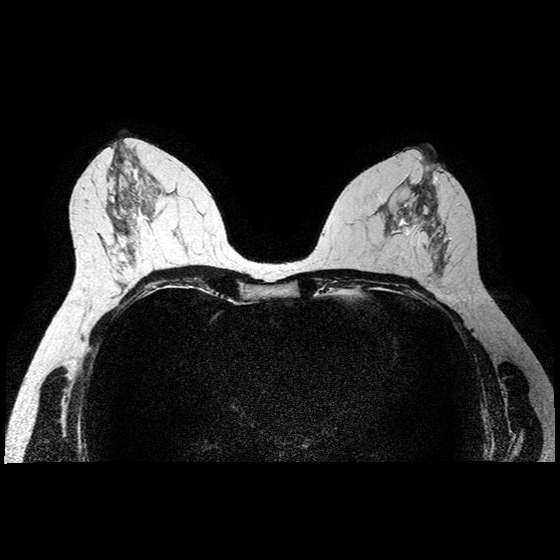
MRI of the breasts; 2 images, each one mid-volume slice chosen by position. Age decade 40s.
Image 1: axial T2-weighted / STIR image, series "T2W_TSE SENSE", slice 43 of 84.
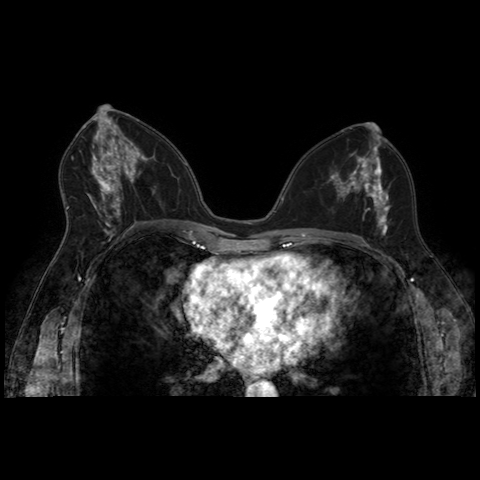
Image 2: post-contrast dynamic axial slice, slice 43 of 84, dynamic phase 5 of 8, 4 mm slice thickness.
MRI impression (as recorded): LEFT BREAST: There is moderate background enhancement. In the leftcentral slightly lateral breast mid depth, 2.4 cm from the nipple and 1.7 cm from the skin there is a 3.4 x 1.5 x 2.3 cm suspiciously enhancing mass seen (volume 2.8 cc), irregularly shaped and spiculated with centrally rapid wash in and washout pattern (Type 3). Posterior tothis dominant lesion there is a second 1.3 x 0.5 x 0.96 cm suspiciously enhancing (Type 3) focus of enhancement seen (5.6 cm from the nipple and 1.9 cm from the skin). Anterior to the dominant lesion there are small areas of suspicious enhancement seen up to 0.9 cm from the nipple. The total anterior posterior extension of the enhancing masses and foci is 5.4 cm in linear order towards the nipple (0.9 cm distance from nipple) and the maximal lateral is 2.5 cm. There is nipple inversion. There is no skin thickening, or left axillary lymphadenopathy present. Benign up to 8 mm simple cysts.
RIGHT BREAST: There is moderate background enhancement. No foci of suspicious enhancement, masses, or areas of architectural distortion seen within the right breast. There is no skin thickening, nipple inversion, or right axillary lymphadenopathy present. Benign simple up to 12 mm cysts. IMPRESSION: 1) 3.5 cm suspicious mass in the left central breast. In addition second 1.3 cm focus of suspicious enhancement posterior to the dominant lesion, as detailed above. Total anterior posterior extension of enhancing mass smaller foci is 5.4 cm towards the nipple (9 mm) in linear configuration - and maximal lateral extension is 2.5 cm (significant images and detailed portfolio with post processed images are saved on PACS for review; raw images: series 705 slice location 84-100).) 2) Left nipple inversion. 3) No axillary lymphadenopathy, no evidence for pectoral muscle involvement. 4) No evidence of contralateral disease; BI-RADS 5.
Pathology recorded for this patient (not read from these images): pathology diagnosis: INVASIVE LOBULAR CARCINOMA. SIZE OF INVASIVE COMPONENT: 4x4x2cm (left breast); pathology report notes: INVASIVE LOBULAR CARCINOMA. SIZE OF INVASIVE COMPONENT: 4x4x2cm HISTOLOGIC MODIFIED SCARF BLOOM RICHARDSON GRADE: I/III LESS THAN 5% OF DUCTAL AND LOBULAR CARCINOMA IN-SITU PRESENT. PERINEURAL INVASION IS PRESENT. MARGINS ARE NEGATIVE FOR CARCINOMA. INVASIVE LOBULAR CARCINOMA. SIZE OF INVASIVE COMPONENT: 4x4x2cm HISTOLOGIC MODIFIED SCARF BLOOM RICHARDSON GRADE: I/III LESS THAN 5% OF DUCTAL AND LOBULAR CARCINOMA IN-SITU PRESENT. PERINEURAL INVASION IS PRESENT. MARGINS ARE NEGATIVE FOR CARCINOMA; clinical background (as recorded): 40s-year-old with newly engorged left nipple.